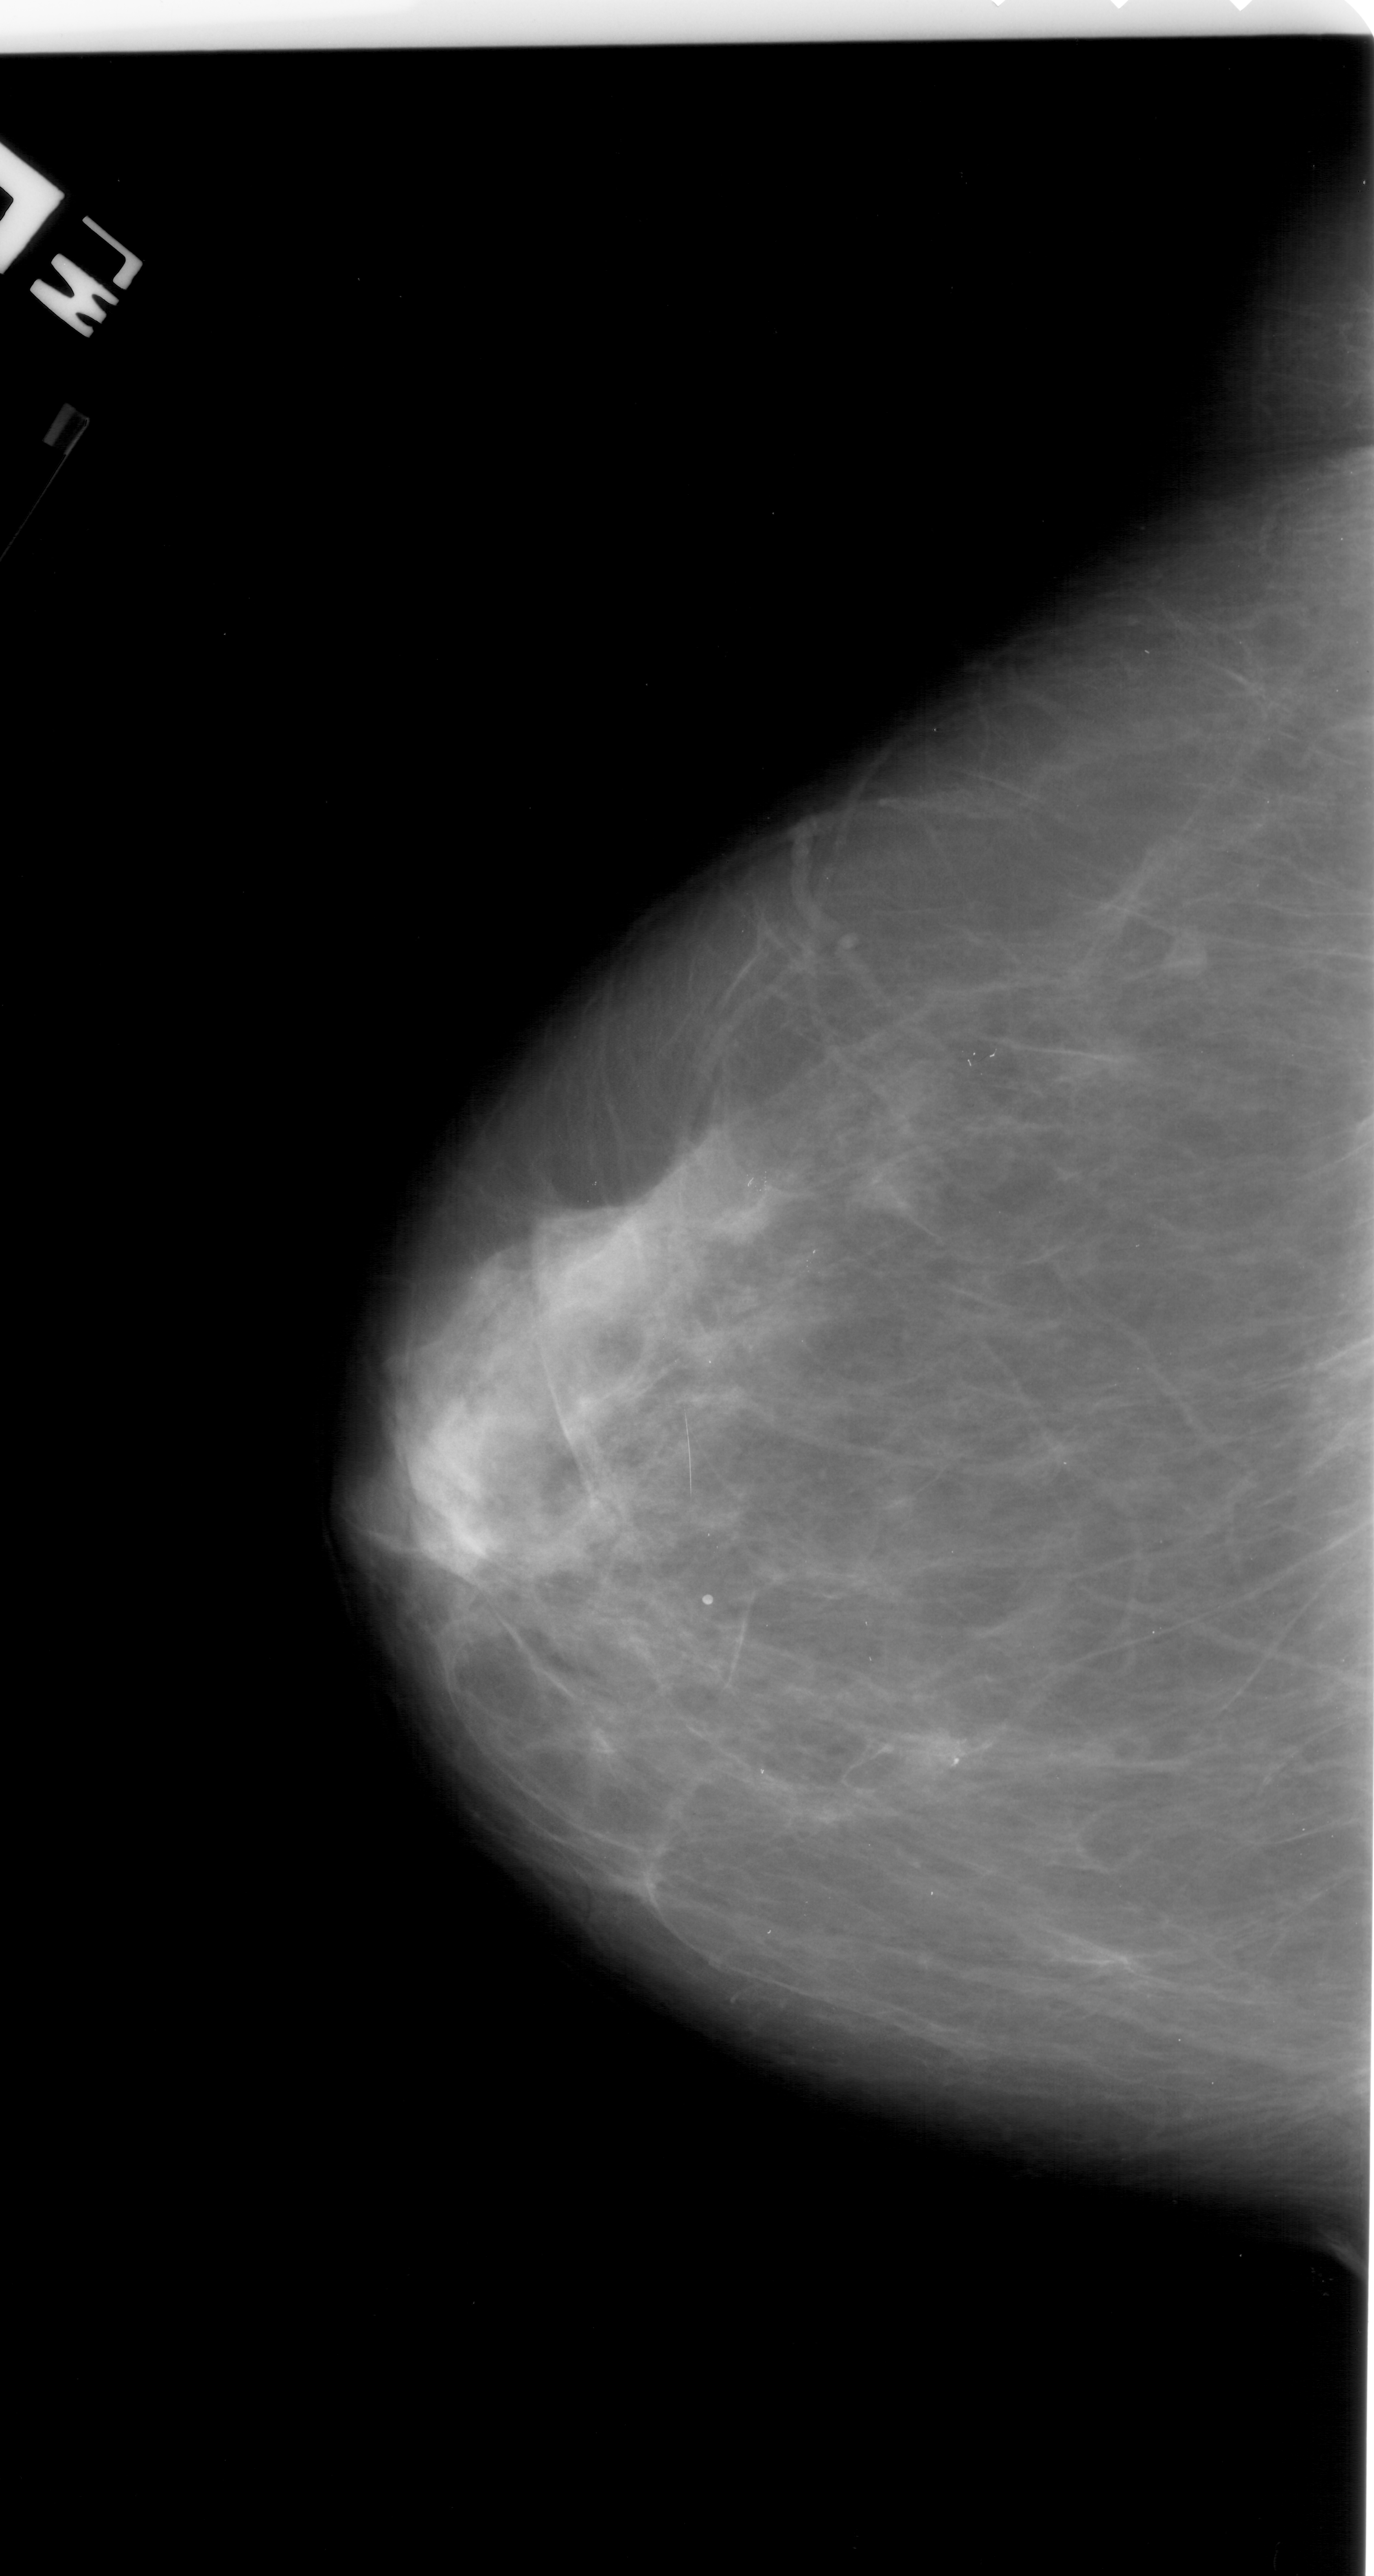
Mammogram (digitized film). Left breast. Craniocaudal (CC) view. Breast composition: scattered fibroglandular densities (BI-RADS density category 2 of 4). 1374 × 2576 image matrix.
Expert-marked regions of interest on this image (one box per marked abnormality):
- calcifications, morphology pleomorphic, distribution linear; BI-RADS assessment category 4; subtlety rating 1 on a 1 (subtle) to 5 (obvious) scale; pathology result (as recorded, not read from the image): malignant: bounding box <919,1731,971,1790> (left, top, right, bottom; pixels)